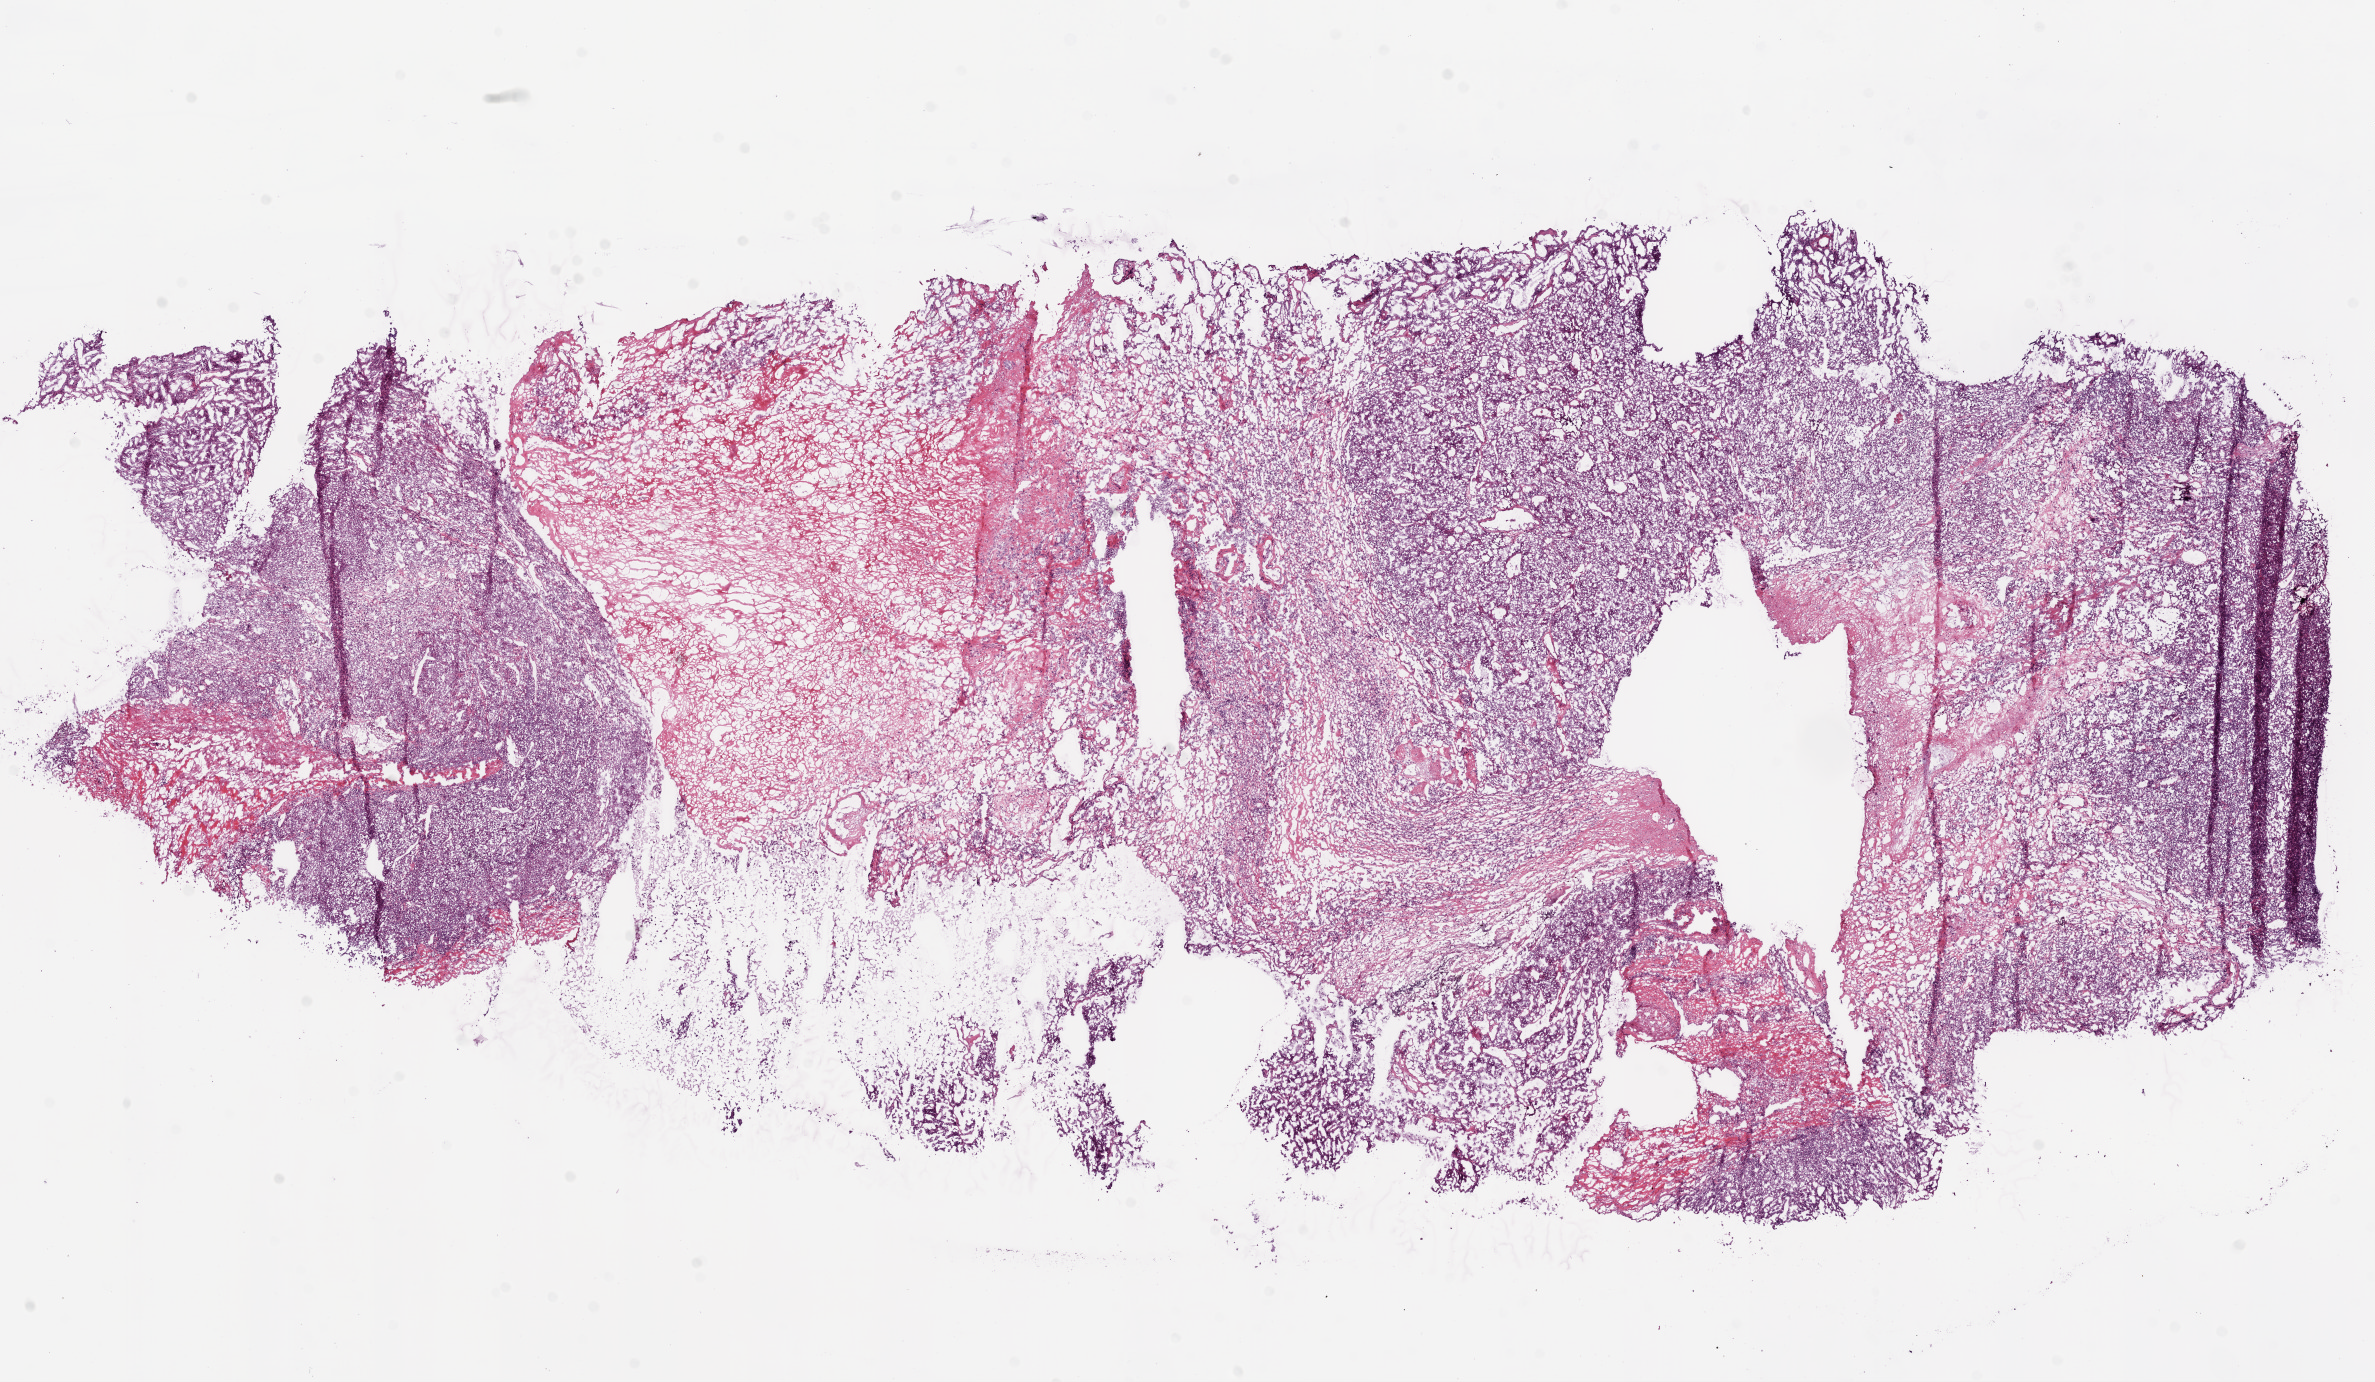
H&E whole-slide image — whole scanned area (about 19.1 x 11.1 mm) shown as a low-resolution overview, frozen section from the bottom of the tissue portion, kidney, primary tumour sample. Patient: female, age at initial diagnosis 69 years. Histologic grade: G4 (undifferentiated). Pathologist review of this section (percent, as recorded): tumour cells 70%, tumour nuclei 75%, normal cells 0%, stromal cells 30%, necrosis 0%.
AJCC pathologic stage: IV. Histologic diagnosis: Clear cell adenocarcinoma, NOS.